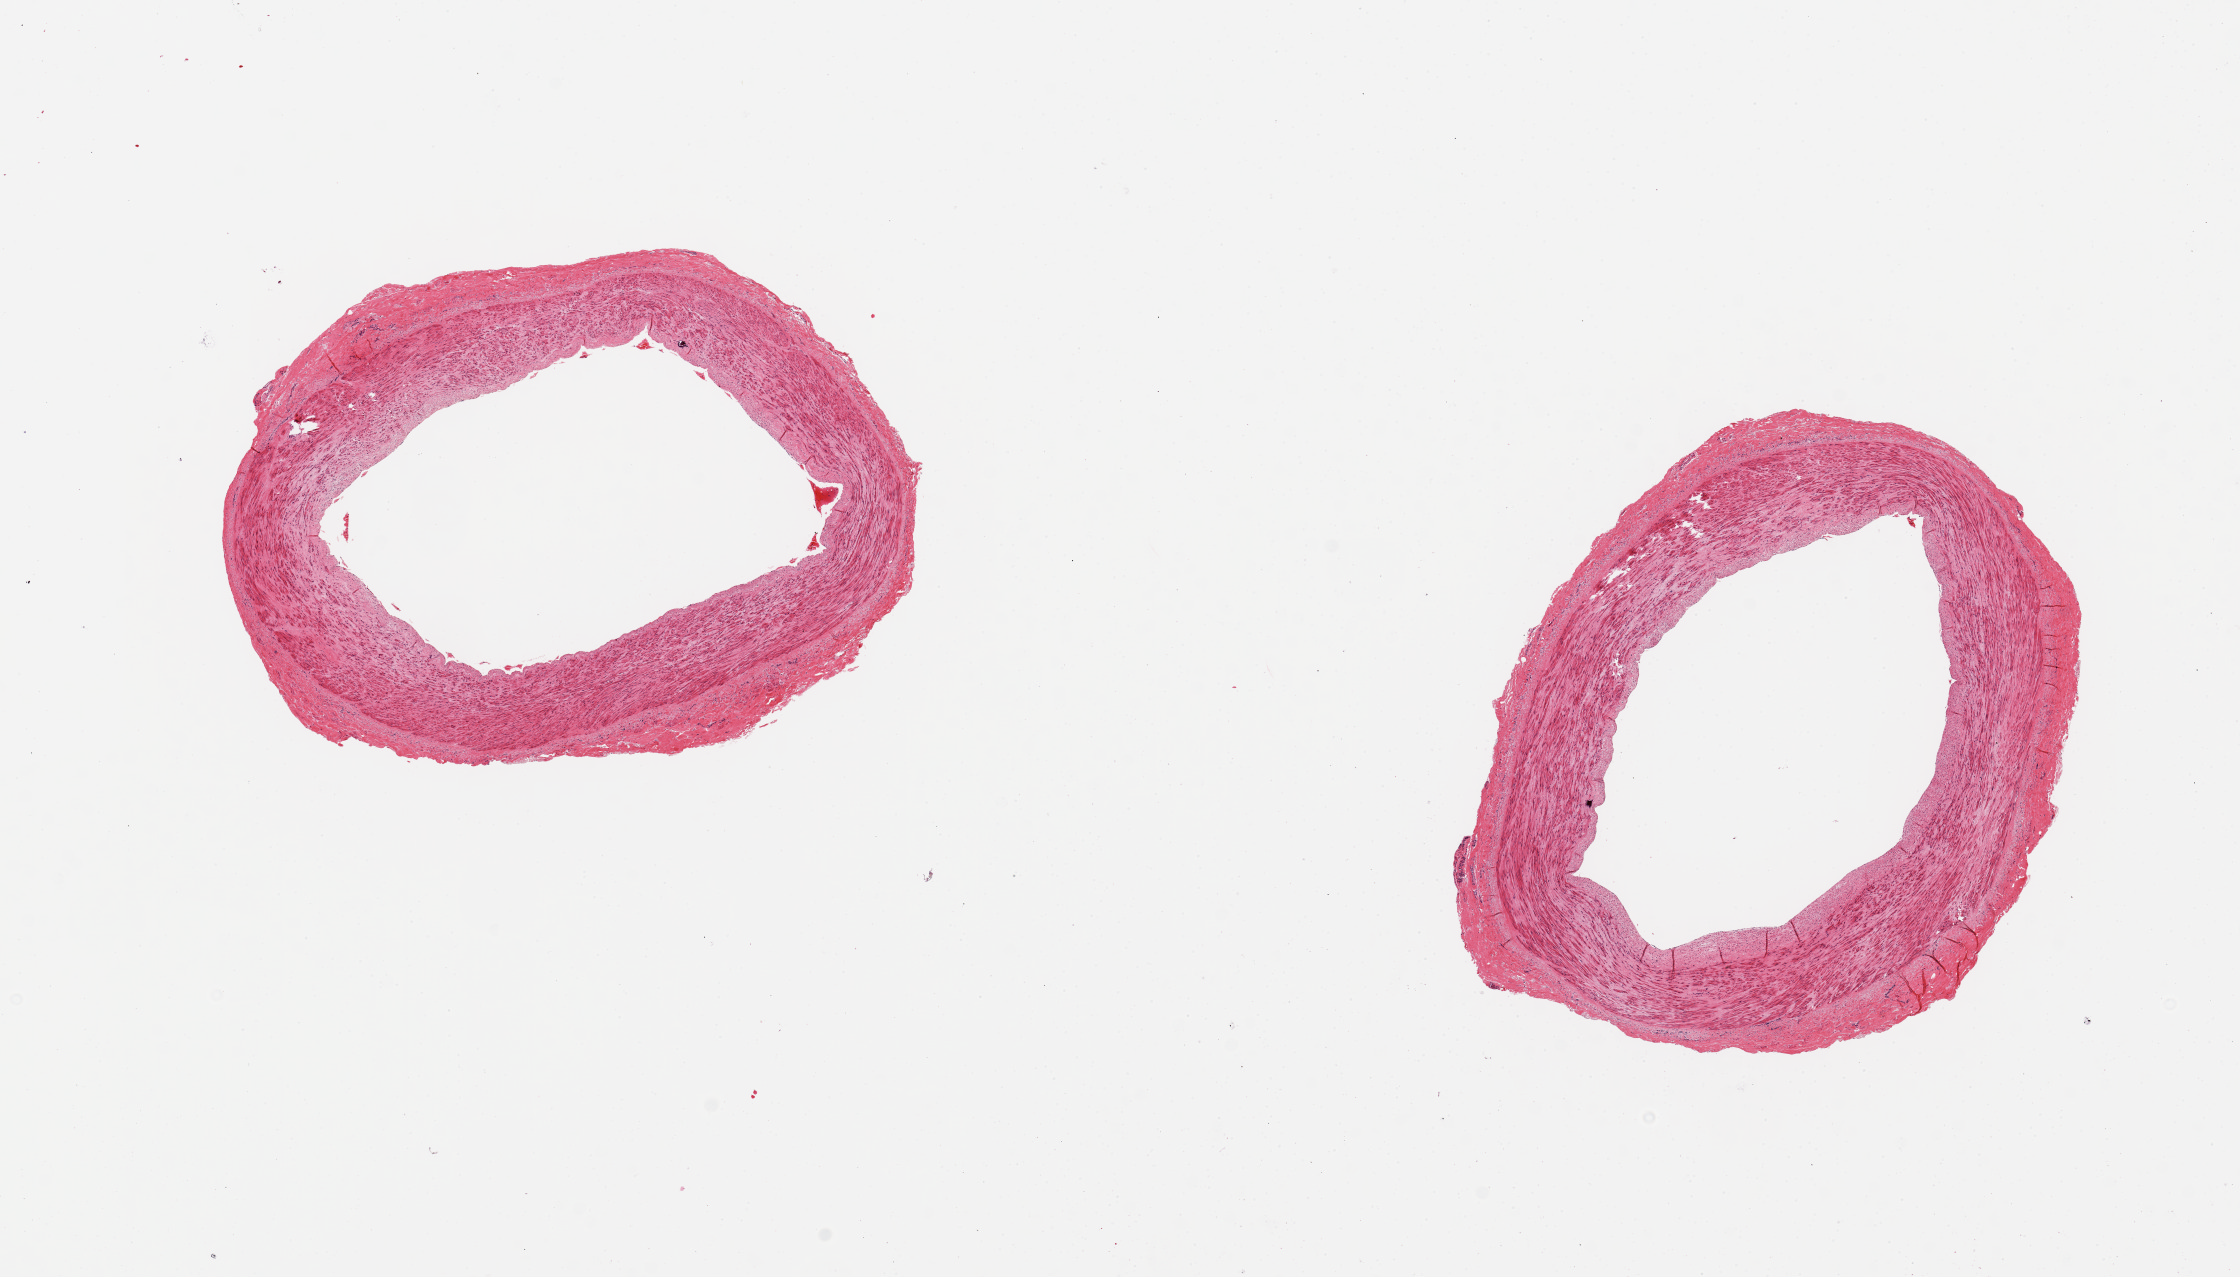
Whole-slide image, haematoxylin and eosin stain, brightfield, a low-resolution overview of the entire scanned area, about 17.7 x 10.1 mm (acquisition: 20x scan); PAXgene-fixed, paraffin-embedded tissue; section of tibial artery (target tissue); tissue donor sample.
Review note (as recorded): 2 pieces; well trimmed, no lesions.